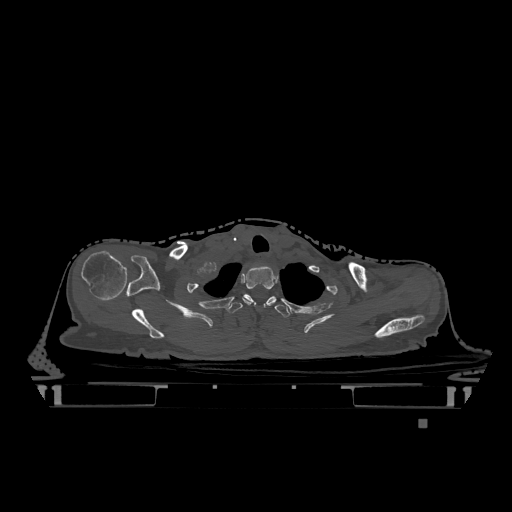
CT including the spine, one axial slice. Slice 984 of 1317 in the series (ordered by position). Bone window (W 1800 / L 400 HU). 512 × 512 image matrix, field of view 500 × 500 mm. Female patient, age 74 years. From the clinical record (not read from this slice): primary cancer: lung; vertebrae with lytic lesions (as recorded): T1, T4, T5, T6, L4, L5.
Structures marked on this image (semi-automatically segmented with operator editing):
- T1 vertebra: bounding box [x1, y1, x2, y2] px = [242, 265, 275, 306]
- T2 vertebra: [227, 294, 290, 318]